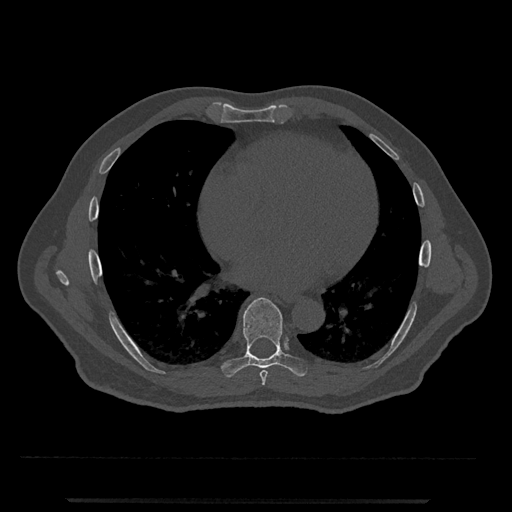
CT including the spine, one axial slice. Slice 635 of 797 in the series (ordered by position). 120 kVp. Bone window (W 1800 / L 400 HU). 0.5 mm slice thickness. 512 × 512 image matrix. Male patient, age 63 years. From the clinical record (not read from this slice): primary cancer: prostate.
Outlined on this slice (semi-automatic segmentation, software-assisted and operator-edited):
- T7 vertebra: bounding box [x1, y1, x2, y2] px = [259, 370, 268, 386]
- T8 vertebra: [221, 297, 307, 377]